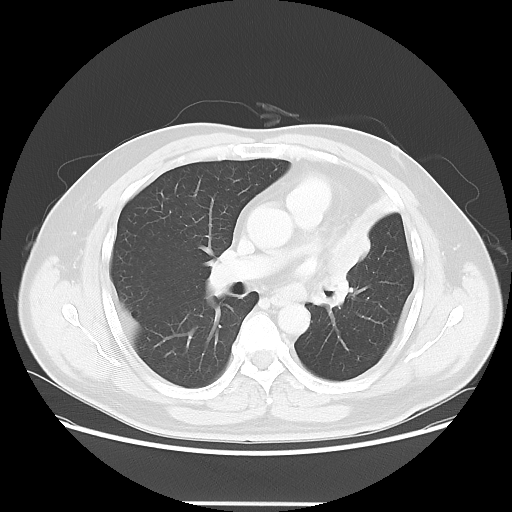
Chest CT, one axial slice. Slice 35 of 62 in the series (ordered by position). Reconstruction kernel LUNG. Lung window (W 1500 / L -600 HU). 512 × 512 image matrix, field of view 403 × 403 mm. Male patient, age 49 years. From the clinical record (not read from this slice): clinical TNM (as recorded): T3 N3 M1c.
Structures marked on this image (bounding box drawn by a radiologist):
- lung tumour (recorded histology: squamous cell carcinoma): box from (x=317, y=219) to (x=382, y=324) px